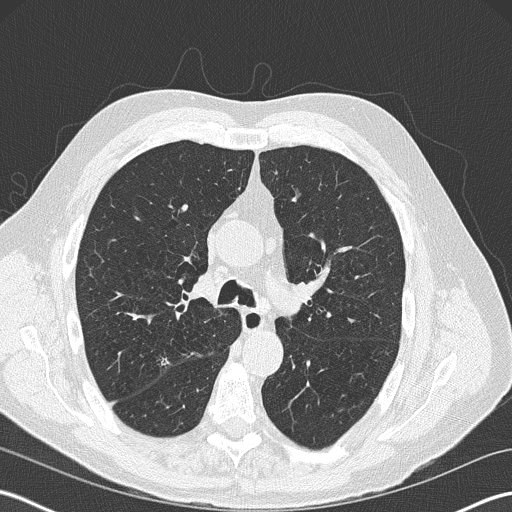
Low-dose screening chest CT, one axial slice. Reconstruction kernel B50f. 120 kVp. Lung window (W 1500 / L -600 HU). 512 × 512 image matrix.
Outlined on this slice (manually delineated by an expert):
- lesion 1 (tumor, upper lobe of right lung): bounding box (x1, y1, x2, y2) in pixels: (153, 351, 172, 370)